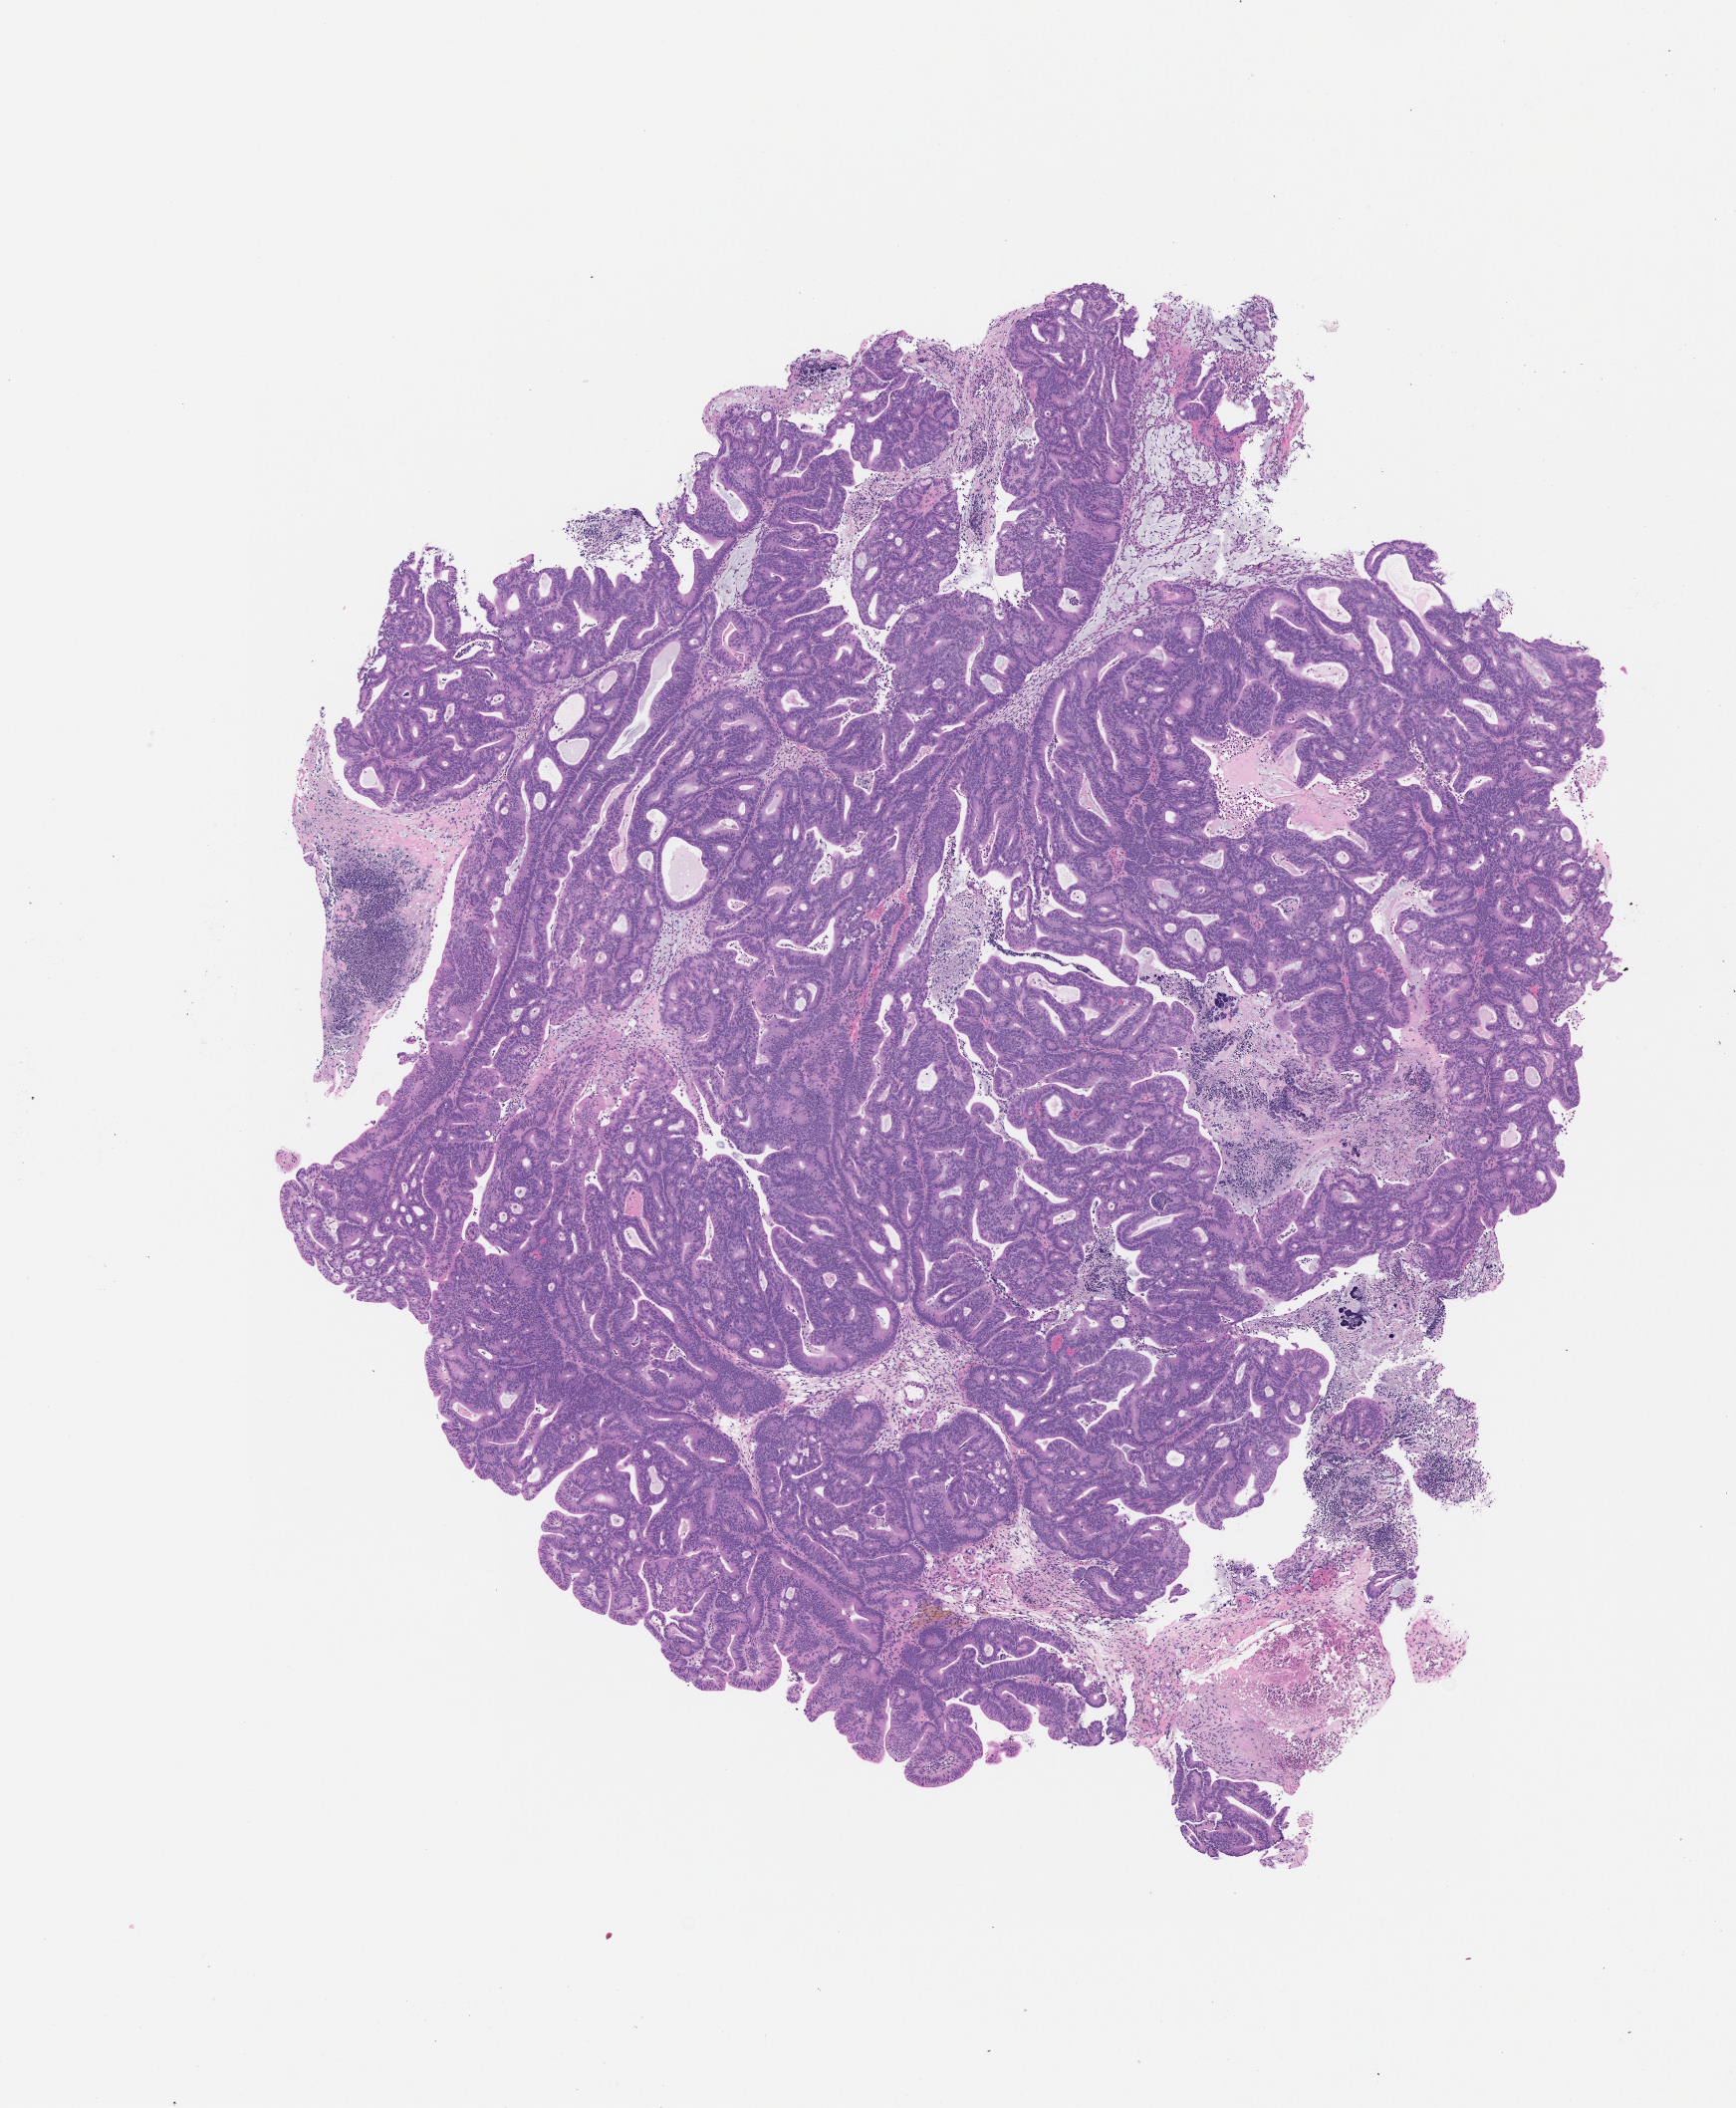
H&E whole-slide image of a patient-derived xenograft (PDX) tumor grown in a mouse, passage 5, whole scanned area (about 7.0 x 8.5 mm) shown as a low-resolution overview, formalin-fixed, paraffin-embedded (FFPE) tissue, tumor site category: colon.
Originating patient diagnosis: Colon Adenocarcinoma.